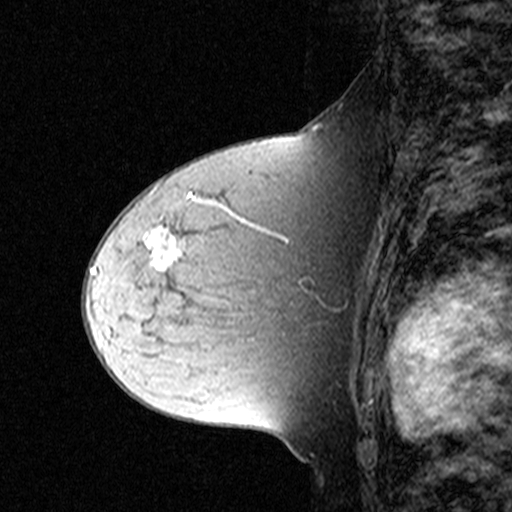
Breast MRI (dynamic contrast-enhanced), one sagittal slice; slice 24 of 44 in the series (ordered by position); dynamic contrast-enhanced study with each time point stored as its own series, time point 2 of 3 at this slice position (early post-contrast, ordered by acquisition time); 1.5 T; TE 4.5 ms, TR 11 ms; 512 × 512 image matrix, field of view 200 × 200 mm. Patient: female, 44 years. Case-level facts recorded for this patient, not image findings: setting: breast cancer imaged before/during neoadjuvant chemotherapy; receptor status: triple-negative.
Outlined on this slice (semi-automatic segmentation, software-assisted and operator-edited):
- analysis volume of interest (the breast-tissue region the enhancement analysis was run in; not a lesion): bounding box [x1, y1, x2, y2] px = [132, 212, 309, 331]
- tumour enhancement mask (voxels above the 90 % enhancement threshold inside the analysis volume of interest): [147, 228, 184, 269]